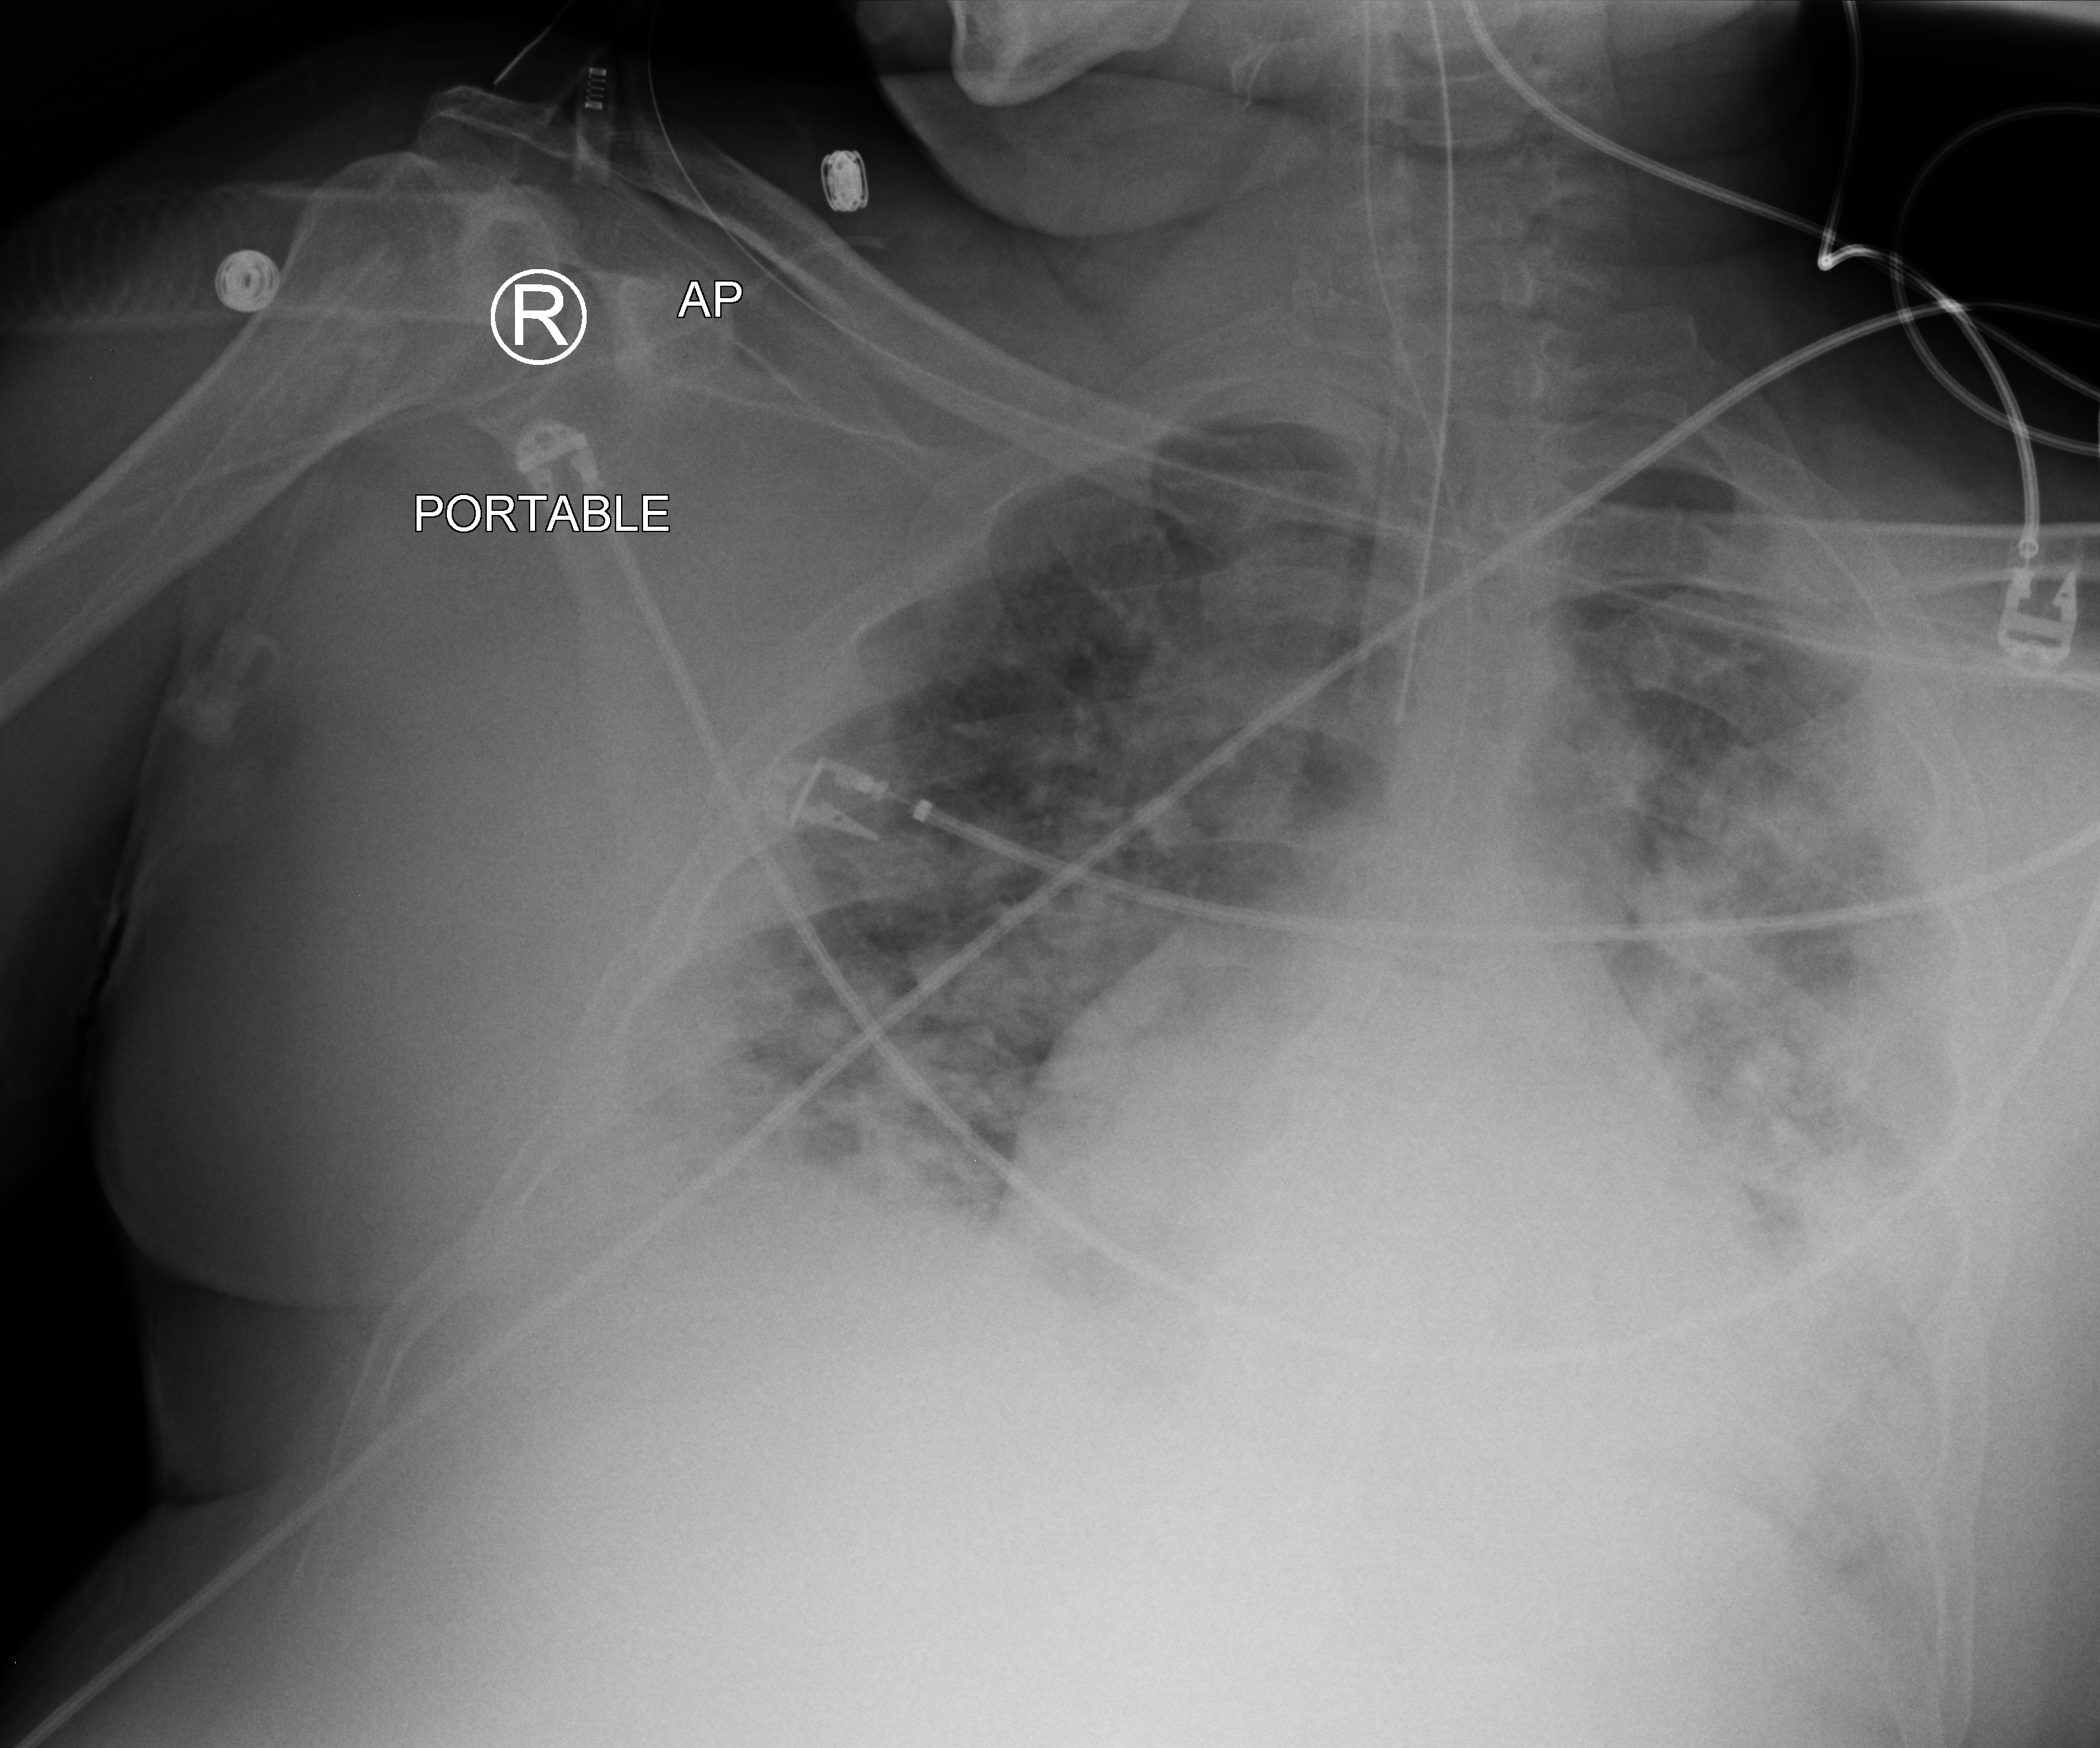
Chest X-ray (portable), anteroposterior (AP) projection. Male patient hospitalised with COVID-19, age 18–59 years.
Admission-level facts for this patient (not findings on this image; timing relative to this image not recorded): chronic kidney disease (admission record): no.